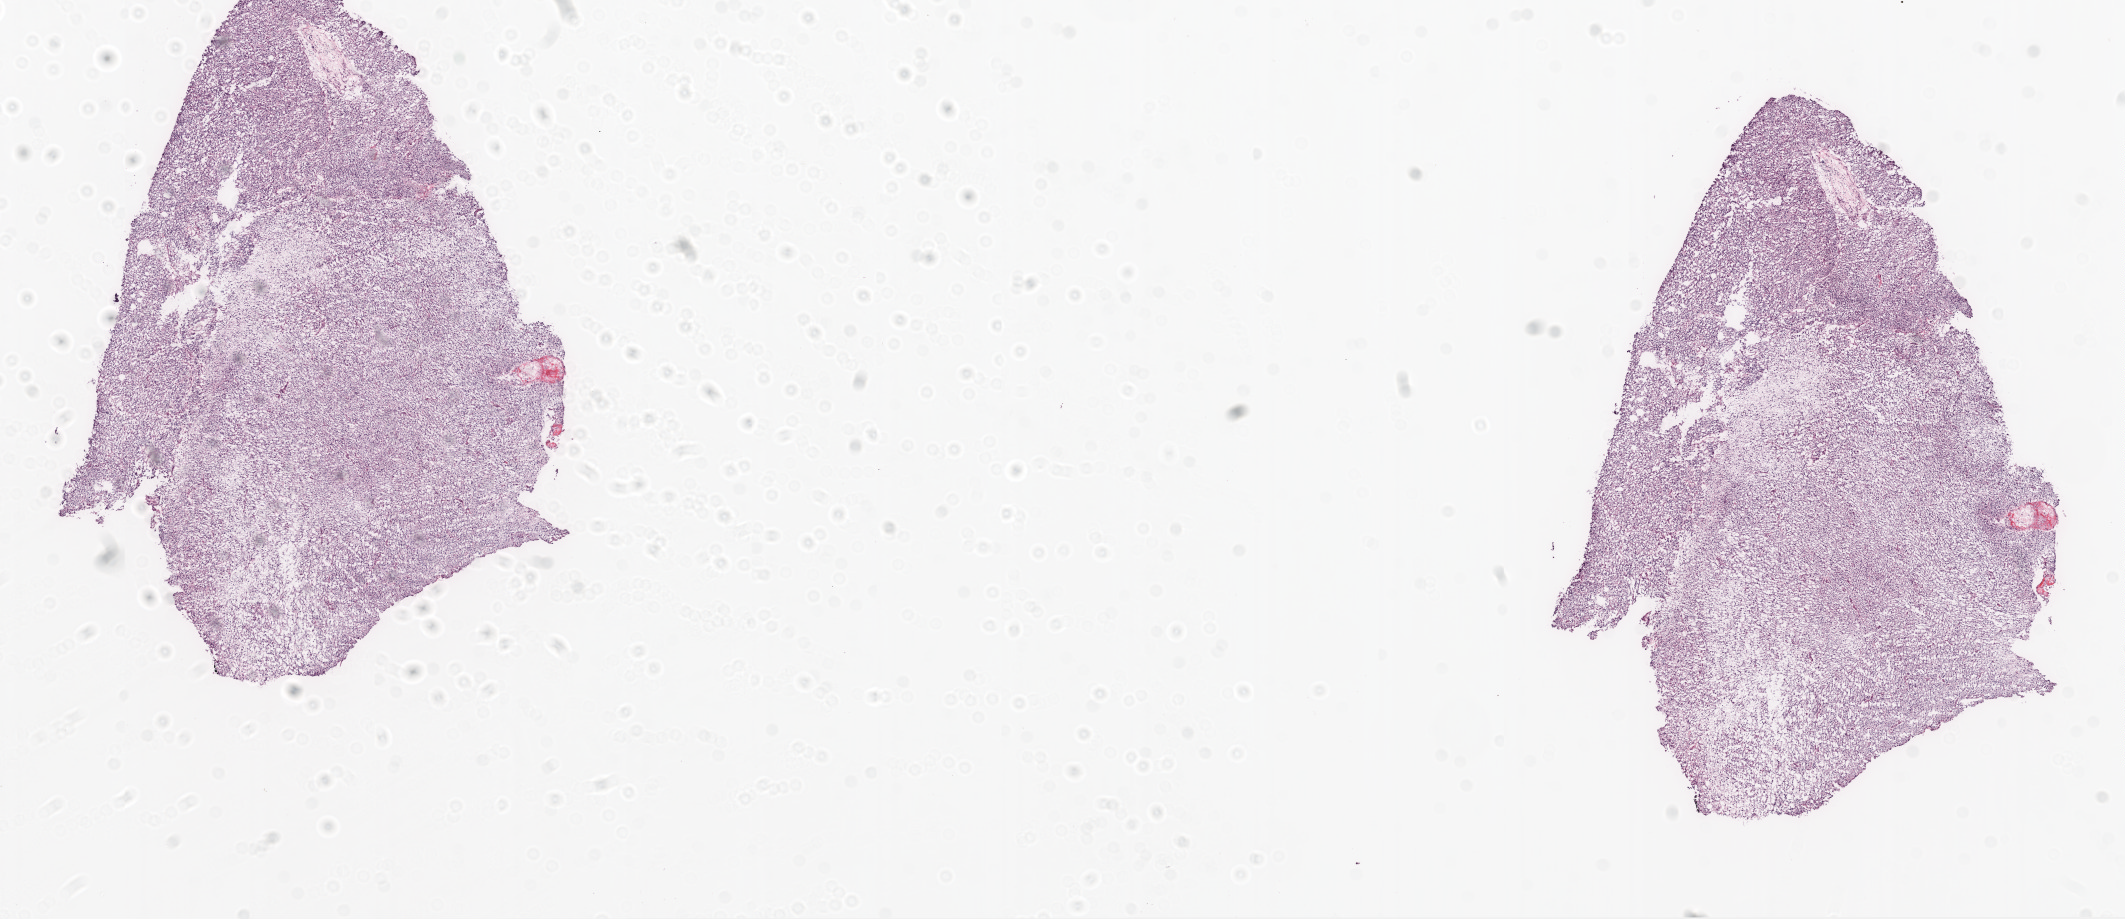
Digitized H&E-stained tissue section (whole slide) — shown as a low-resolution overview of the whole scanned area (about 17.1 x 7.4 mm). Frozen section. Brain, primary tumour sample. Patient: female, age at initial diagnosis 55 years. Slide review estimates, as recorded: tumour cells 100%, tumour nuclei 85%, normal cells 0%, stromal cells 0%, necrosis 0%.
Diagnosis: Glioblastoma.